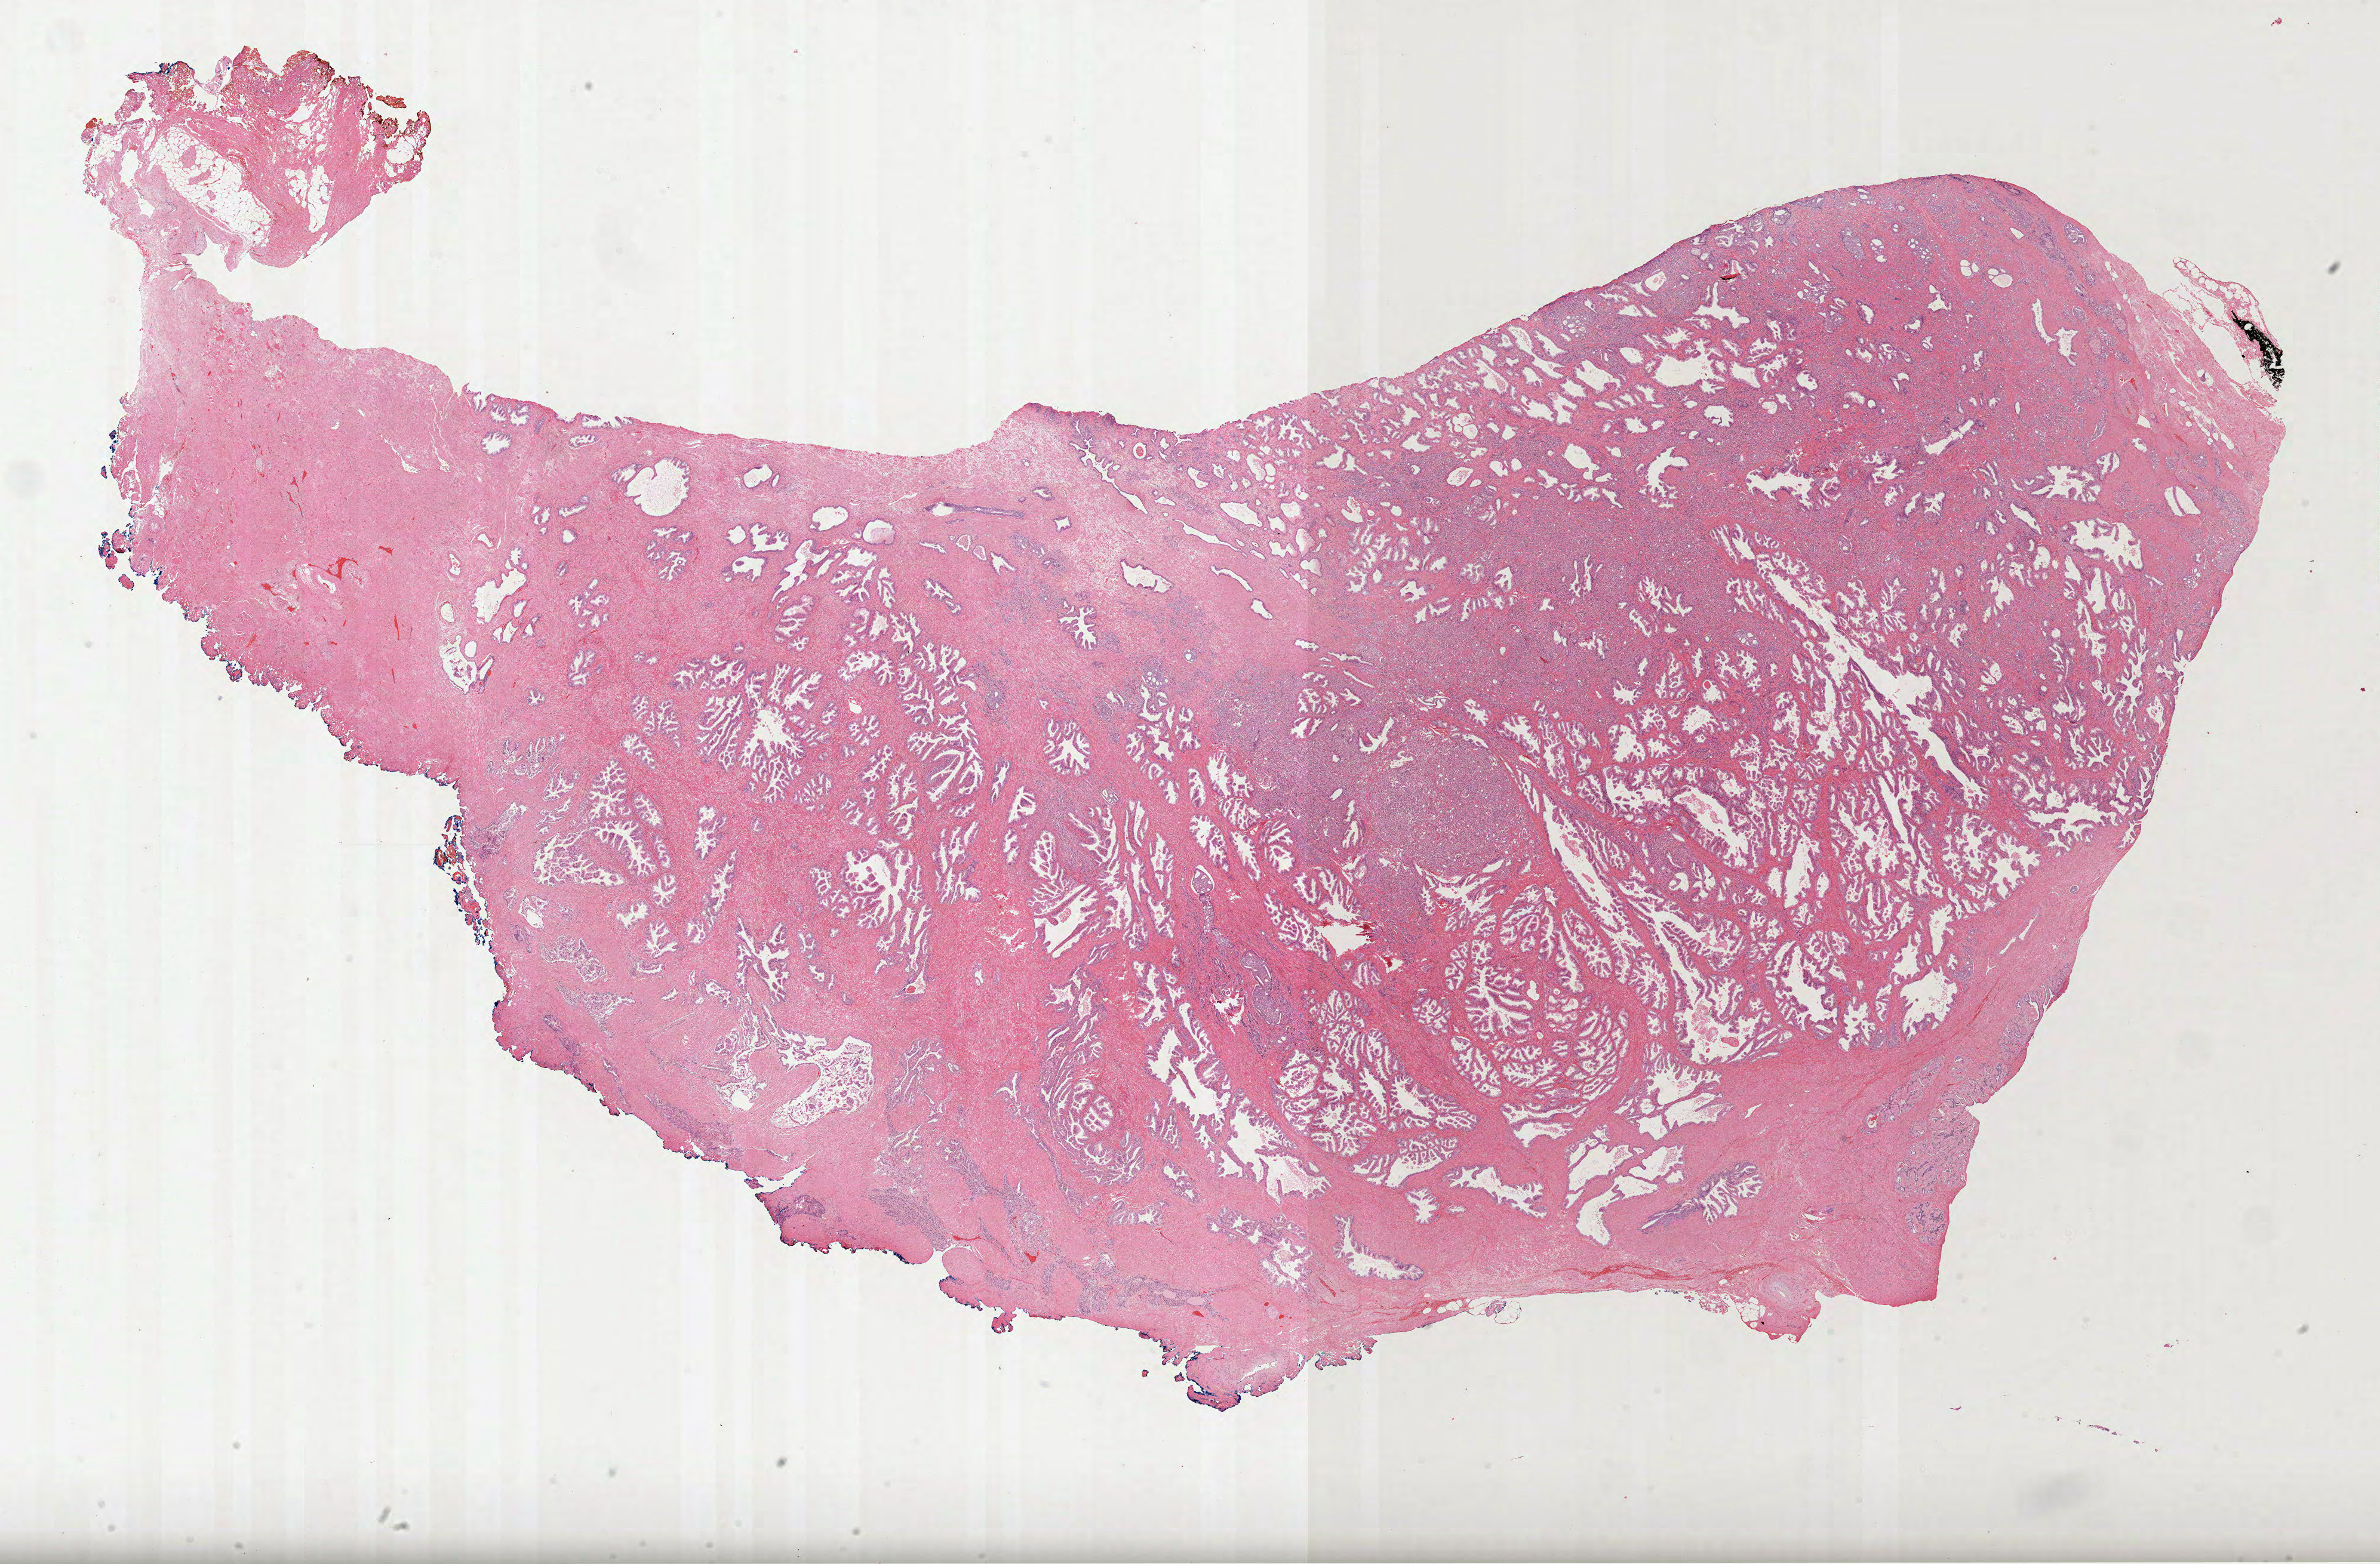
Digitized H&E-stained tissue section (whole slide) — a low-resolution overview of the entire scanned area, about 32.1 x 21.1 mm (acquisition: 40x scan); FFPE section; sample: primary tumour, prostate. Patient: male, age at initial diagnosis 60 years. Gleason score: 9 (4+5).
• lymph nodes positive (case pathology): 0 of 5 examined
• histologic diagnosis: Acinar cell carcinoma (prostate gland)
• laterality: bilateral